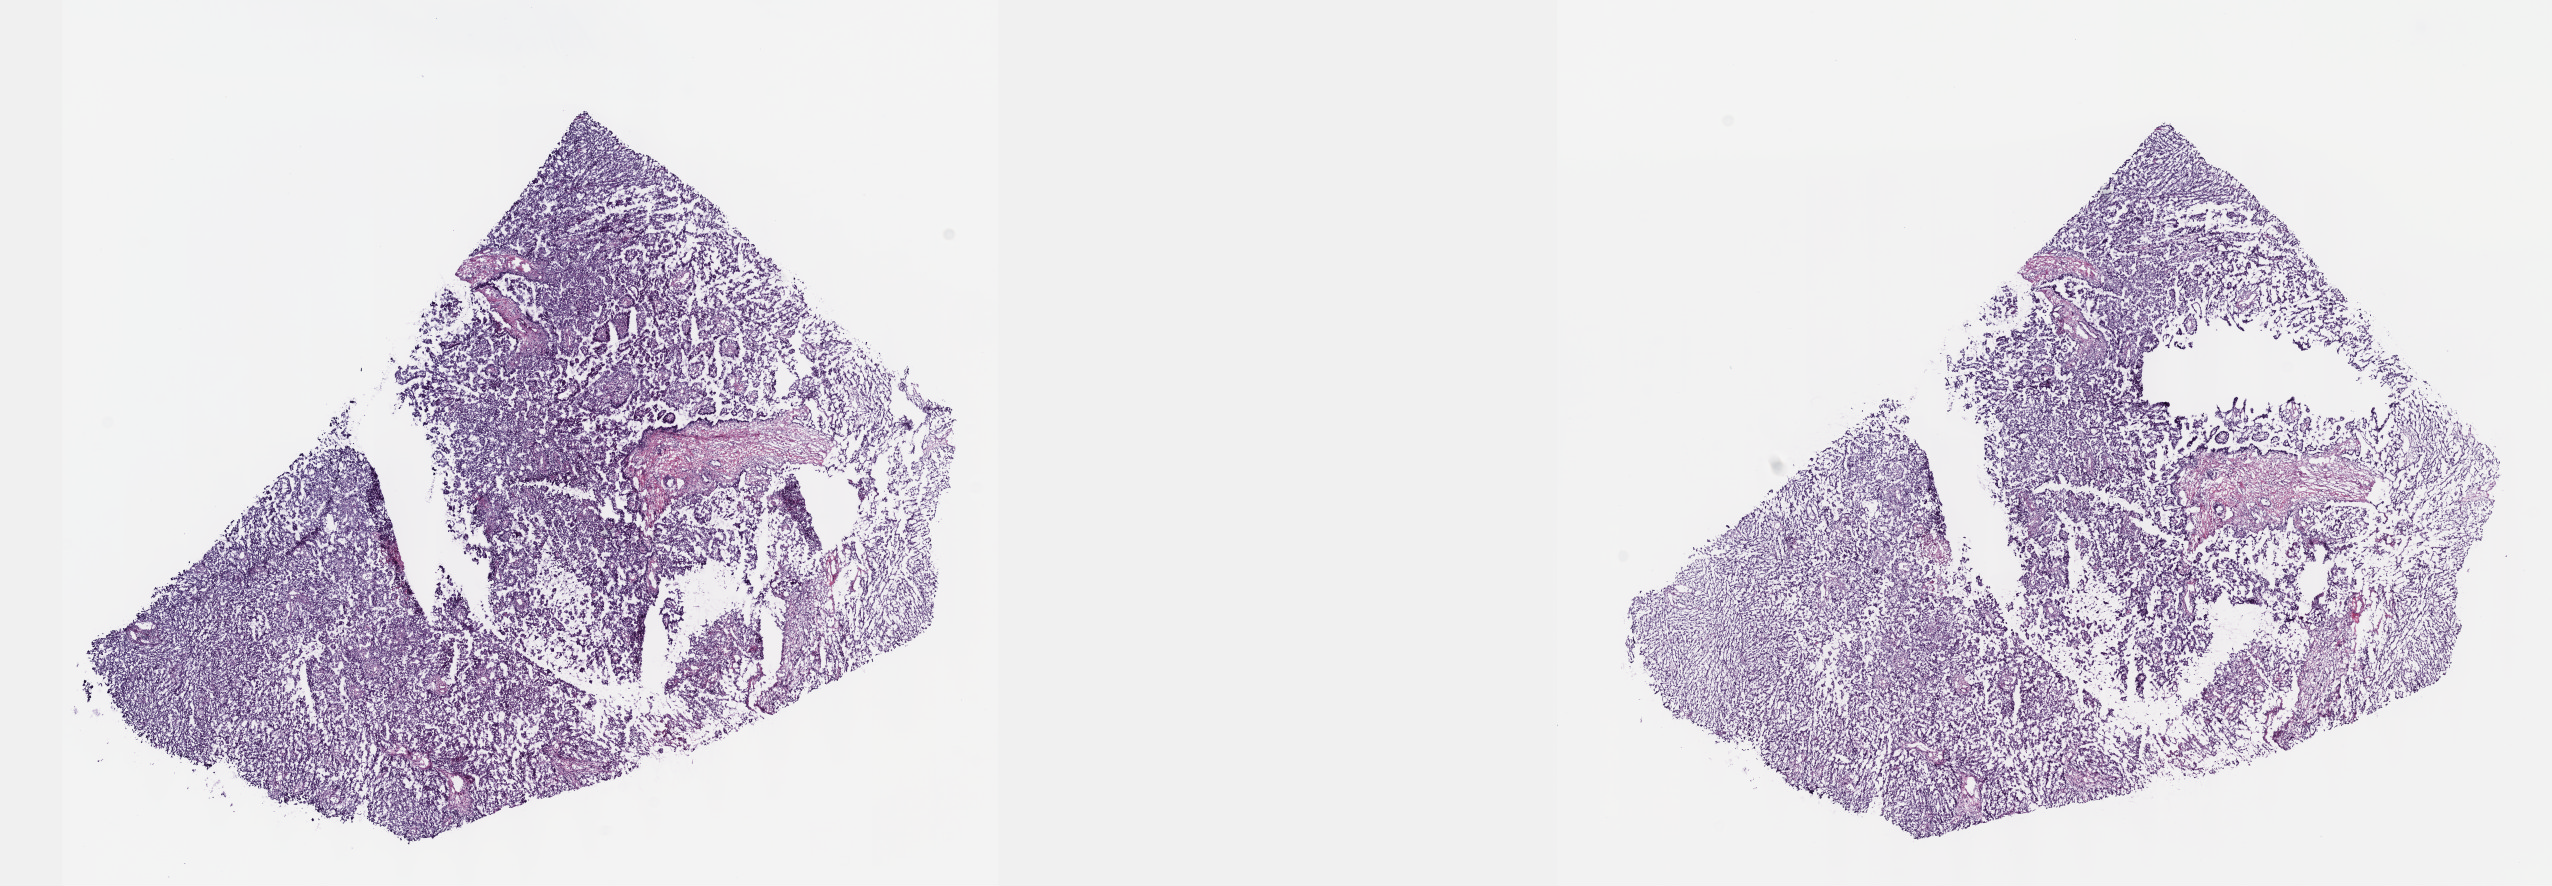
Hematoxylin and eosin (H&E) stained whole-slide image — whole scanned area (about 20.6 x 7.2 mm, acquisition: 40x scan) shown as a low-resolution overview; frozen section from the top of the tissue portion; primary tumour sample from the kidney. Male, age 71 years at initial diagnosis. Pathologist review of this section (percent, as recorded): tumour cells 80%, tumour nuclei 90%, normal cells 0%, stromal cells 15%, necrosis 5%. Infiltration values recorded for this section: lymphocyte infiltration 8%, monocyte infiltration 0%, neutrophil infiltration 1%.
- diagnosis: Papillary adenocarcinoma, NOS
- AJCC pathologic stage: III
- laterality: left